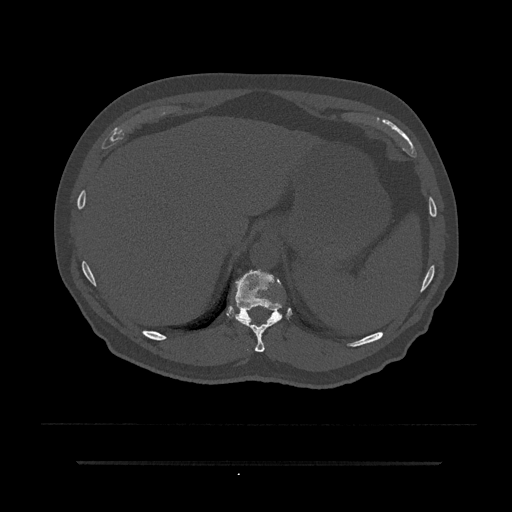
CT including the spine, one axial slice; slice 298 of 797 in the series (ordered by position); reconstruction kernel Br40s/3; 120 kVp; bone window (W 1800 / L 400 HU); 0.5 mm slice thickness; 512 × 512 image matrix, field of view 464 × 464 mm. Patient: male, 59 years. Case-level facts recorded for this patient, not image findings: primary cancer: bile ducts; vertebrae with lytic lesions (as recorded): T10.
Structures marked on this image (semi-automatic segmentation, software-assisted and operator-edited):
- T10 vertebra: box from (x=235, y=290) to (x=282, y=352) px
- T11 vertebra: (x=229, y=270)–(x=289, y=323)